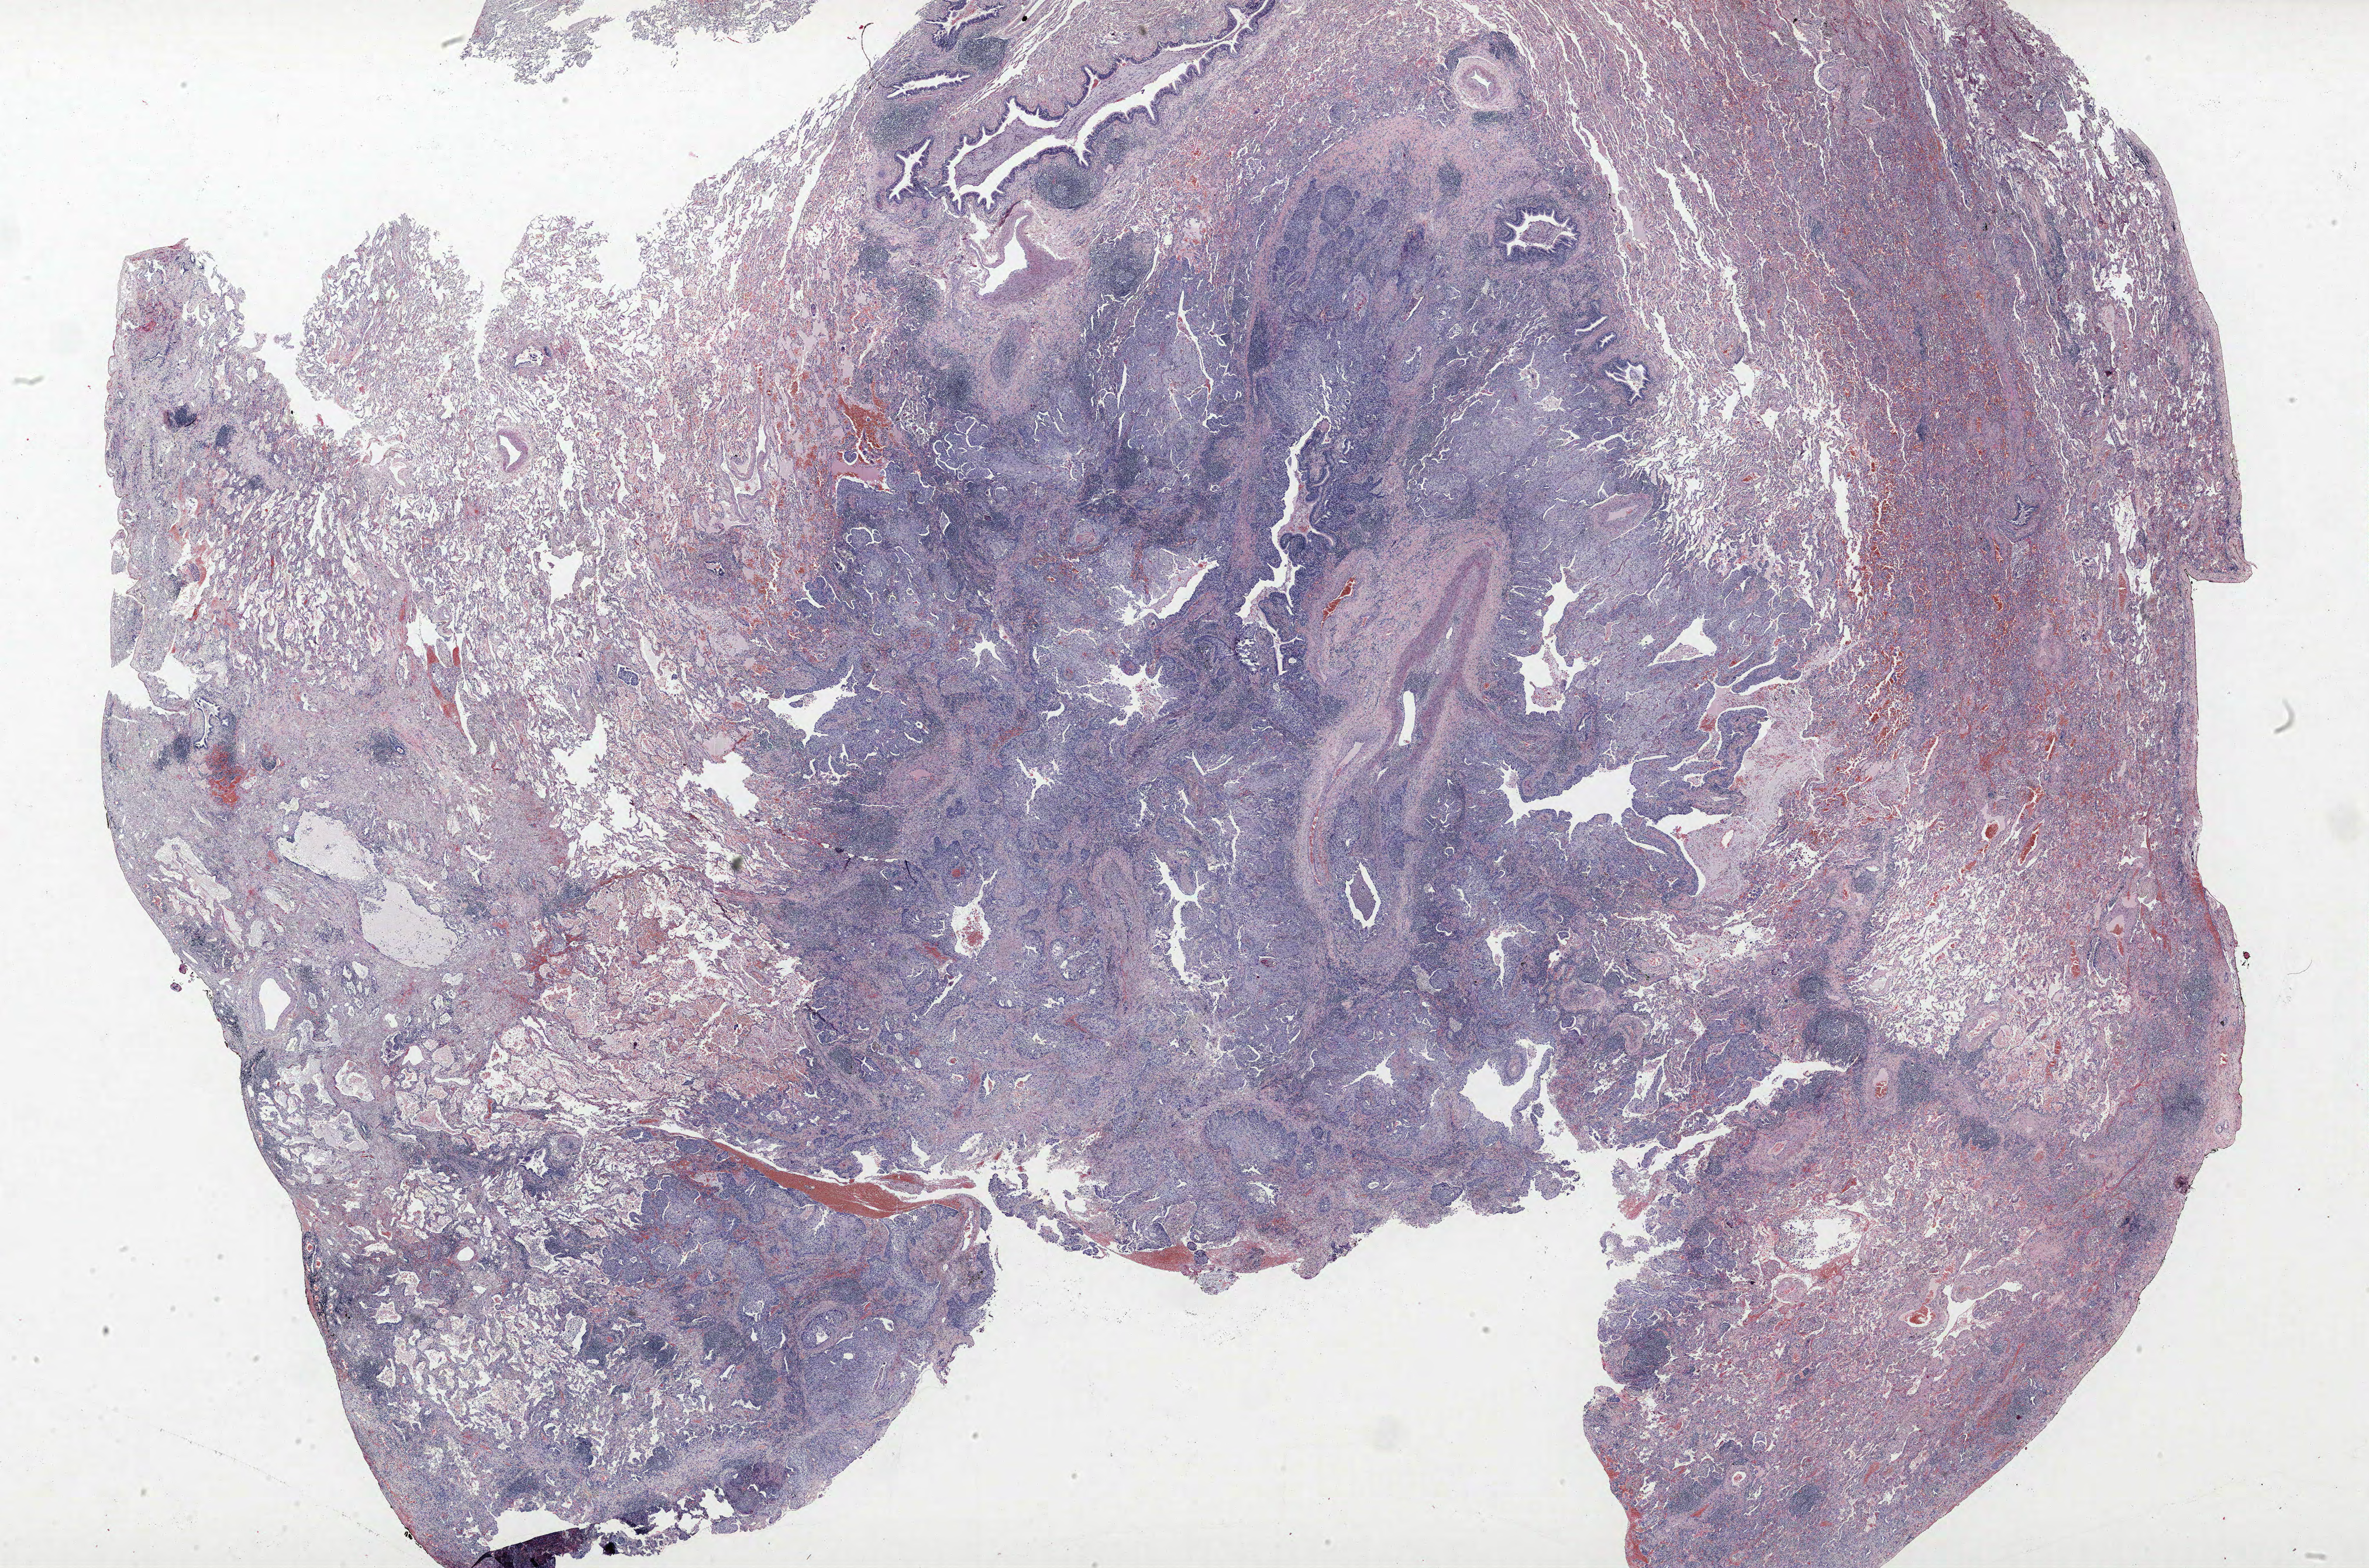
Hematoxylin and eosin (H&E) stained whole-slide image, low-resolution overview of the scanned area, about 32.4 x 21.5 mm (from a 40x scan); formalin-fixed paraffin-embedded (FFPE) section; lung tissue. Male, age 64 at enrolment. Current smoker at enrolment. Grade: moderately differentiated (G2).
* ICD-O-3 topography: upper lobe of lung (C34.1)
* primary tumour location (clinical record): right upper lobe
* stage (AJCC 6th edition): IIB
* participant's lung-cancer diagnosis: Squamous cell carcinoma, NOS
* tumour size (pathology): 21 mm